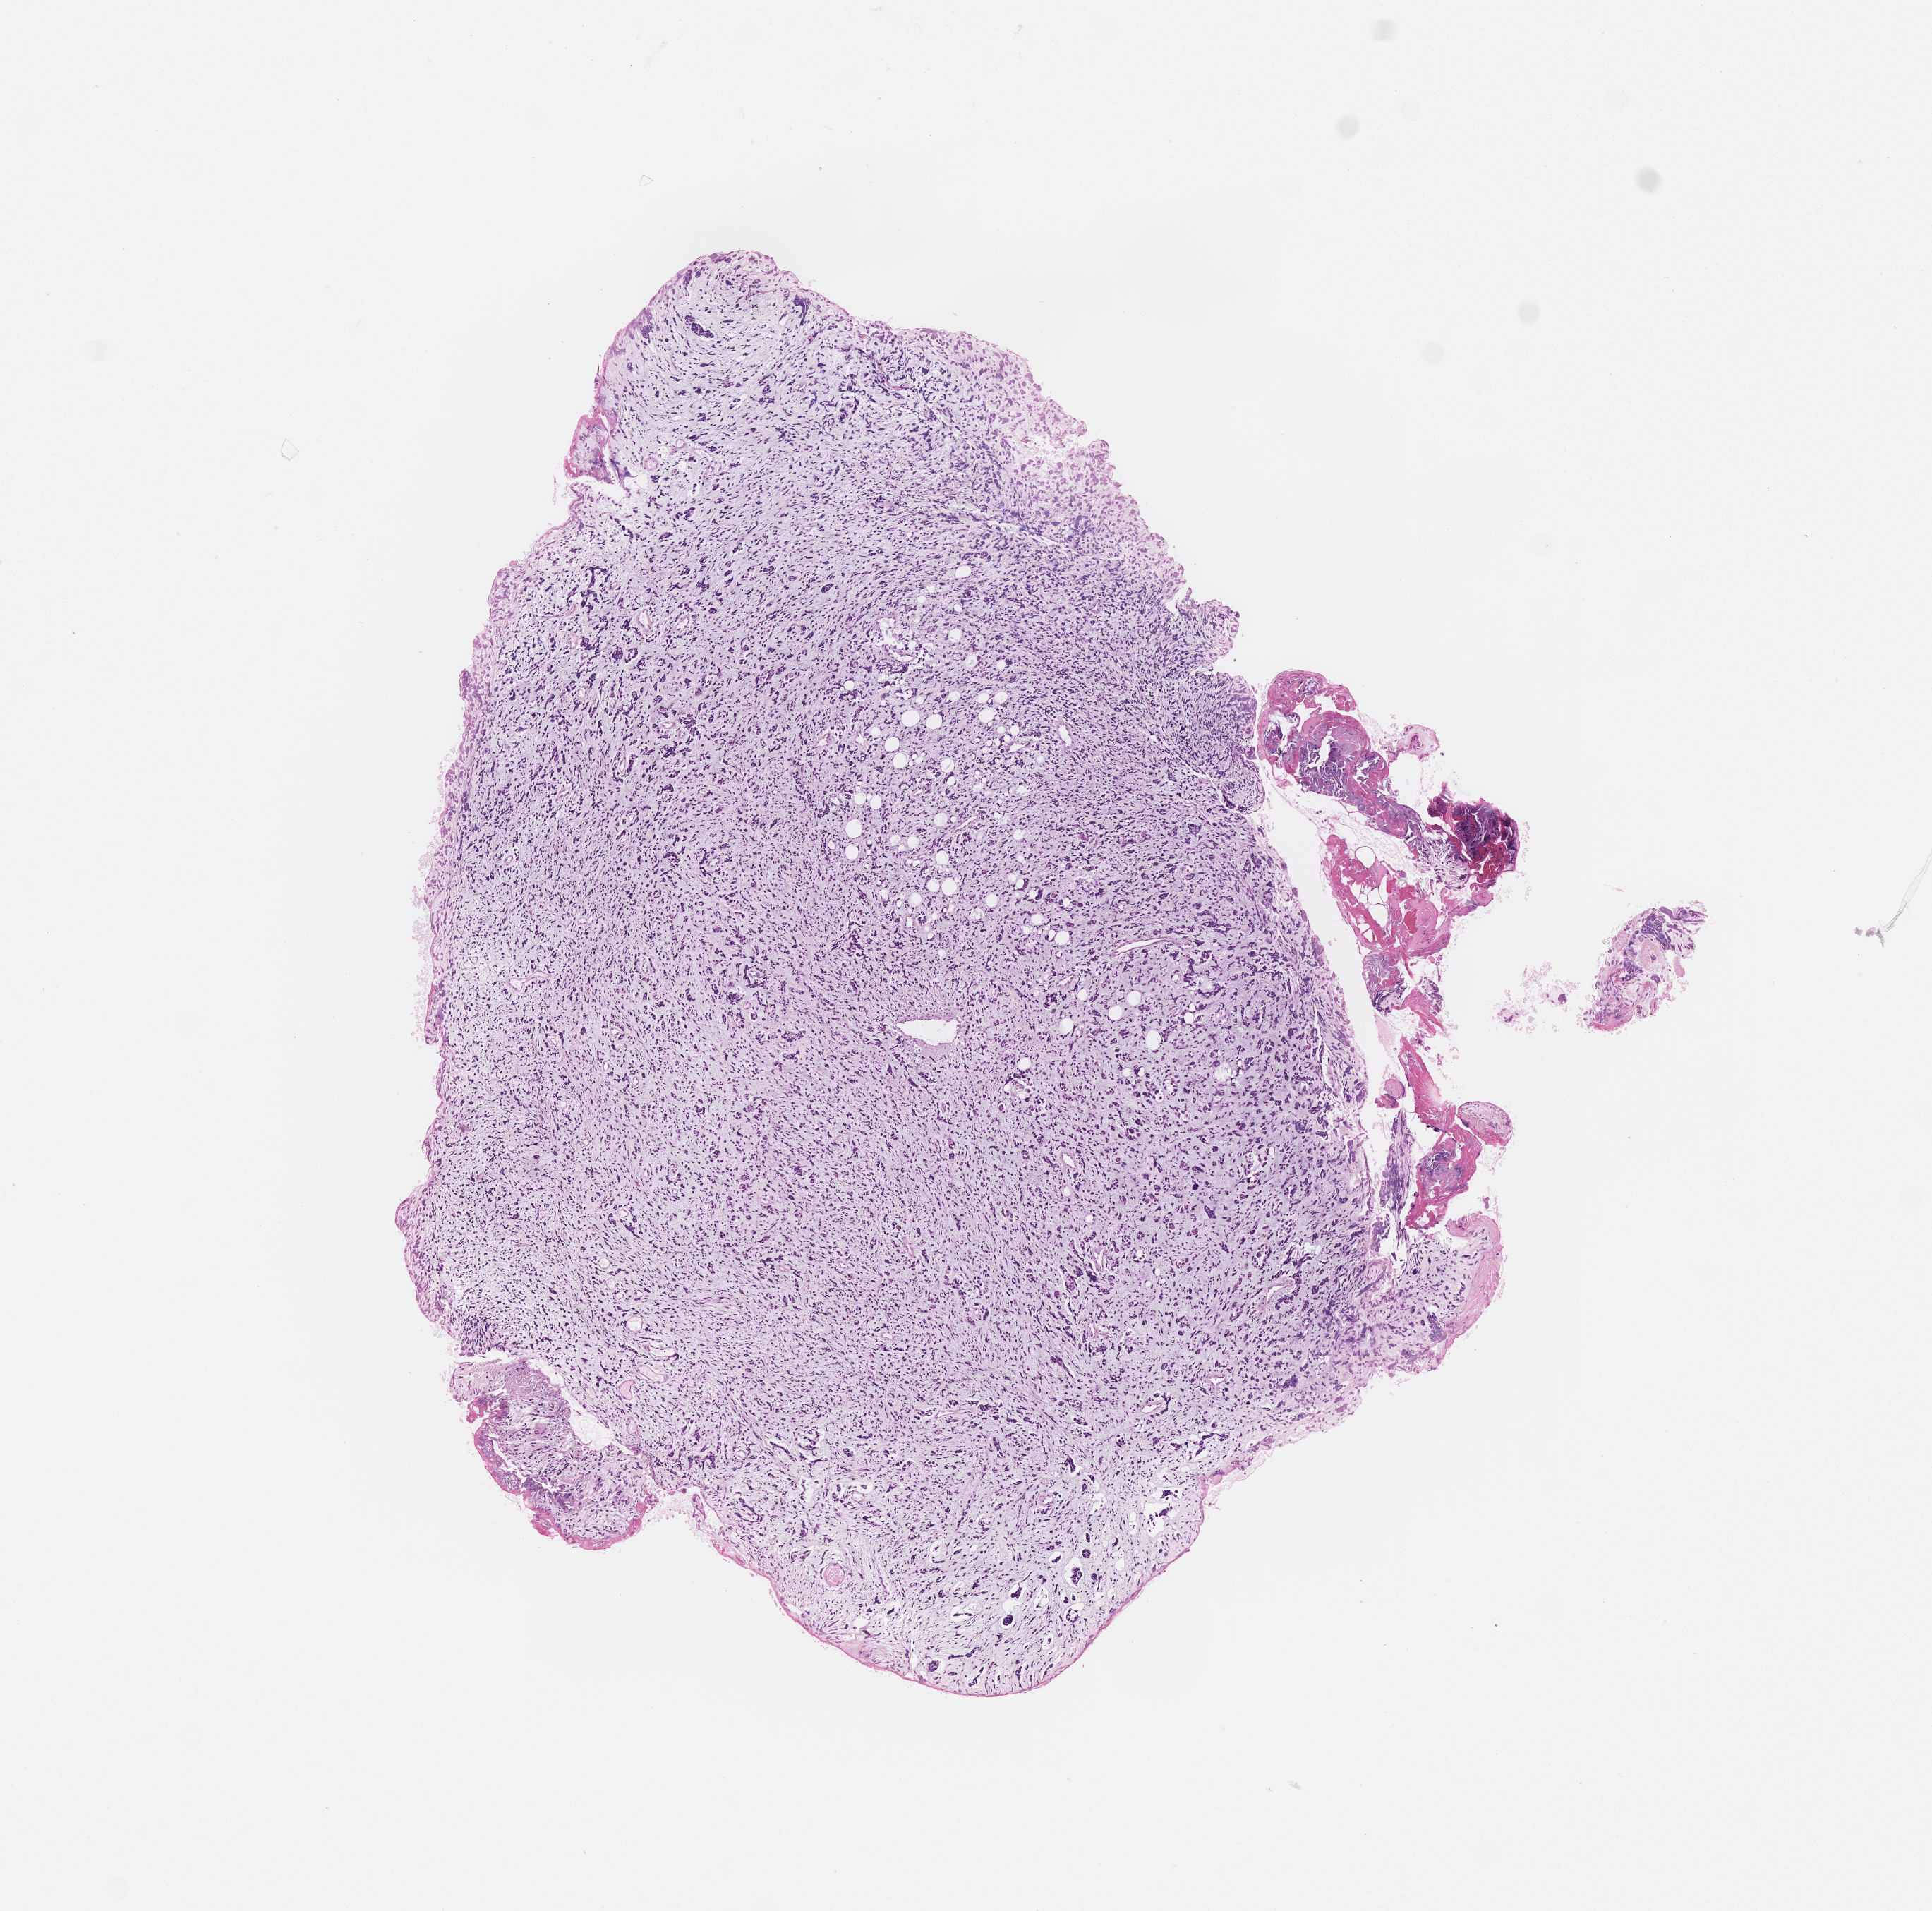
Whole-slide image, hematoxylin and eosin (H&E) stain of tumor tissue — whole scanned area (about 5.5 x 5.5 mm) shown as a low-resolution overview. FFPE section. Site: prostate. Patient: male, age 8.4 years at diagnosis.
- diagnosis: rhabdomyosarcoma; histological classification: embryonal rhabdomyosarcoma with diffuse anaplasia
- metastatic status at presentation (as recorded): metastatic (confirmed)
- stage (as recorded): 4